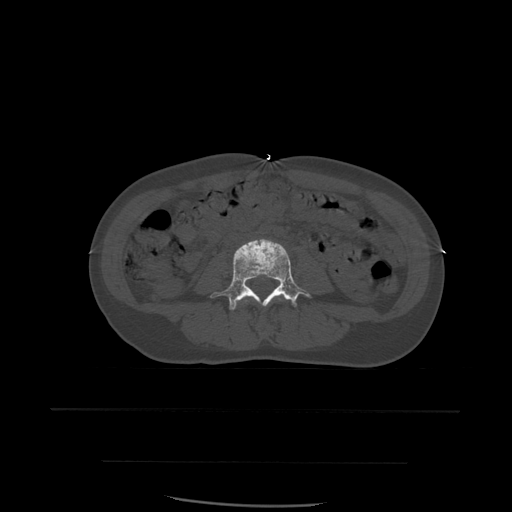
CT including the spine, one axial slice; bone window (W 1800 / L 400 HU); 512 × 512 image matrix, field of view 392 × 392 mm. Patient age 48 years. Case-level facts recorded for this patient, not image findings: primary cancer: lung.
Annotated regions visible in this slice (semi-automatic segmentation, software-assisted and operator-edited):
- L3 vertebra: bounding box [x1, y1, x2, y2] px = [241, 297, 286, 306]
- L4 vertebra: [211, 239, 310, 311]